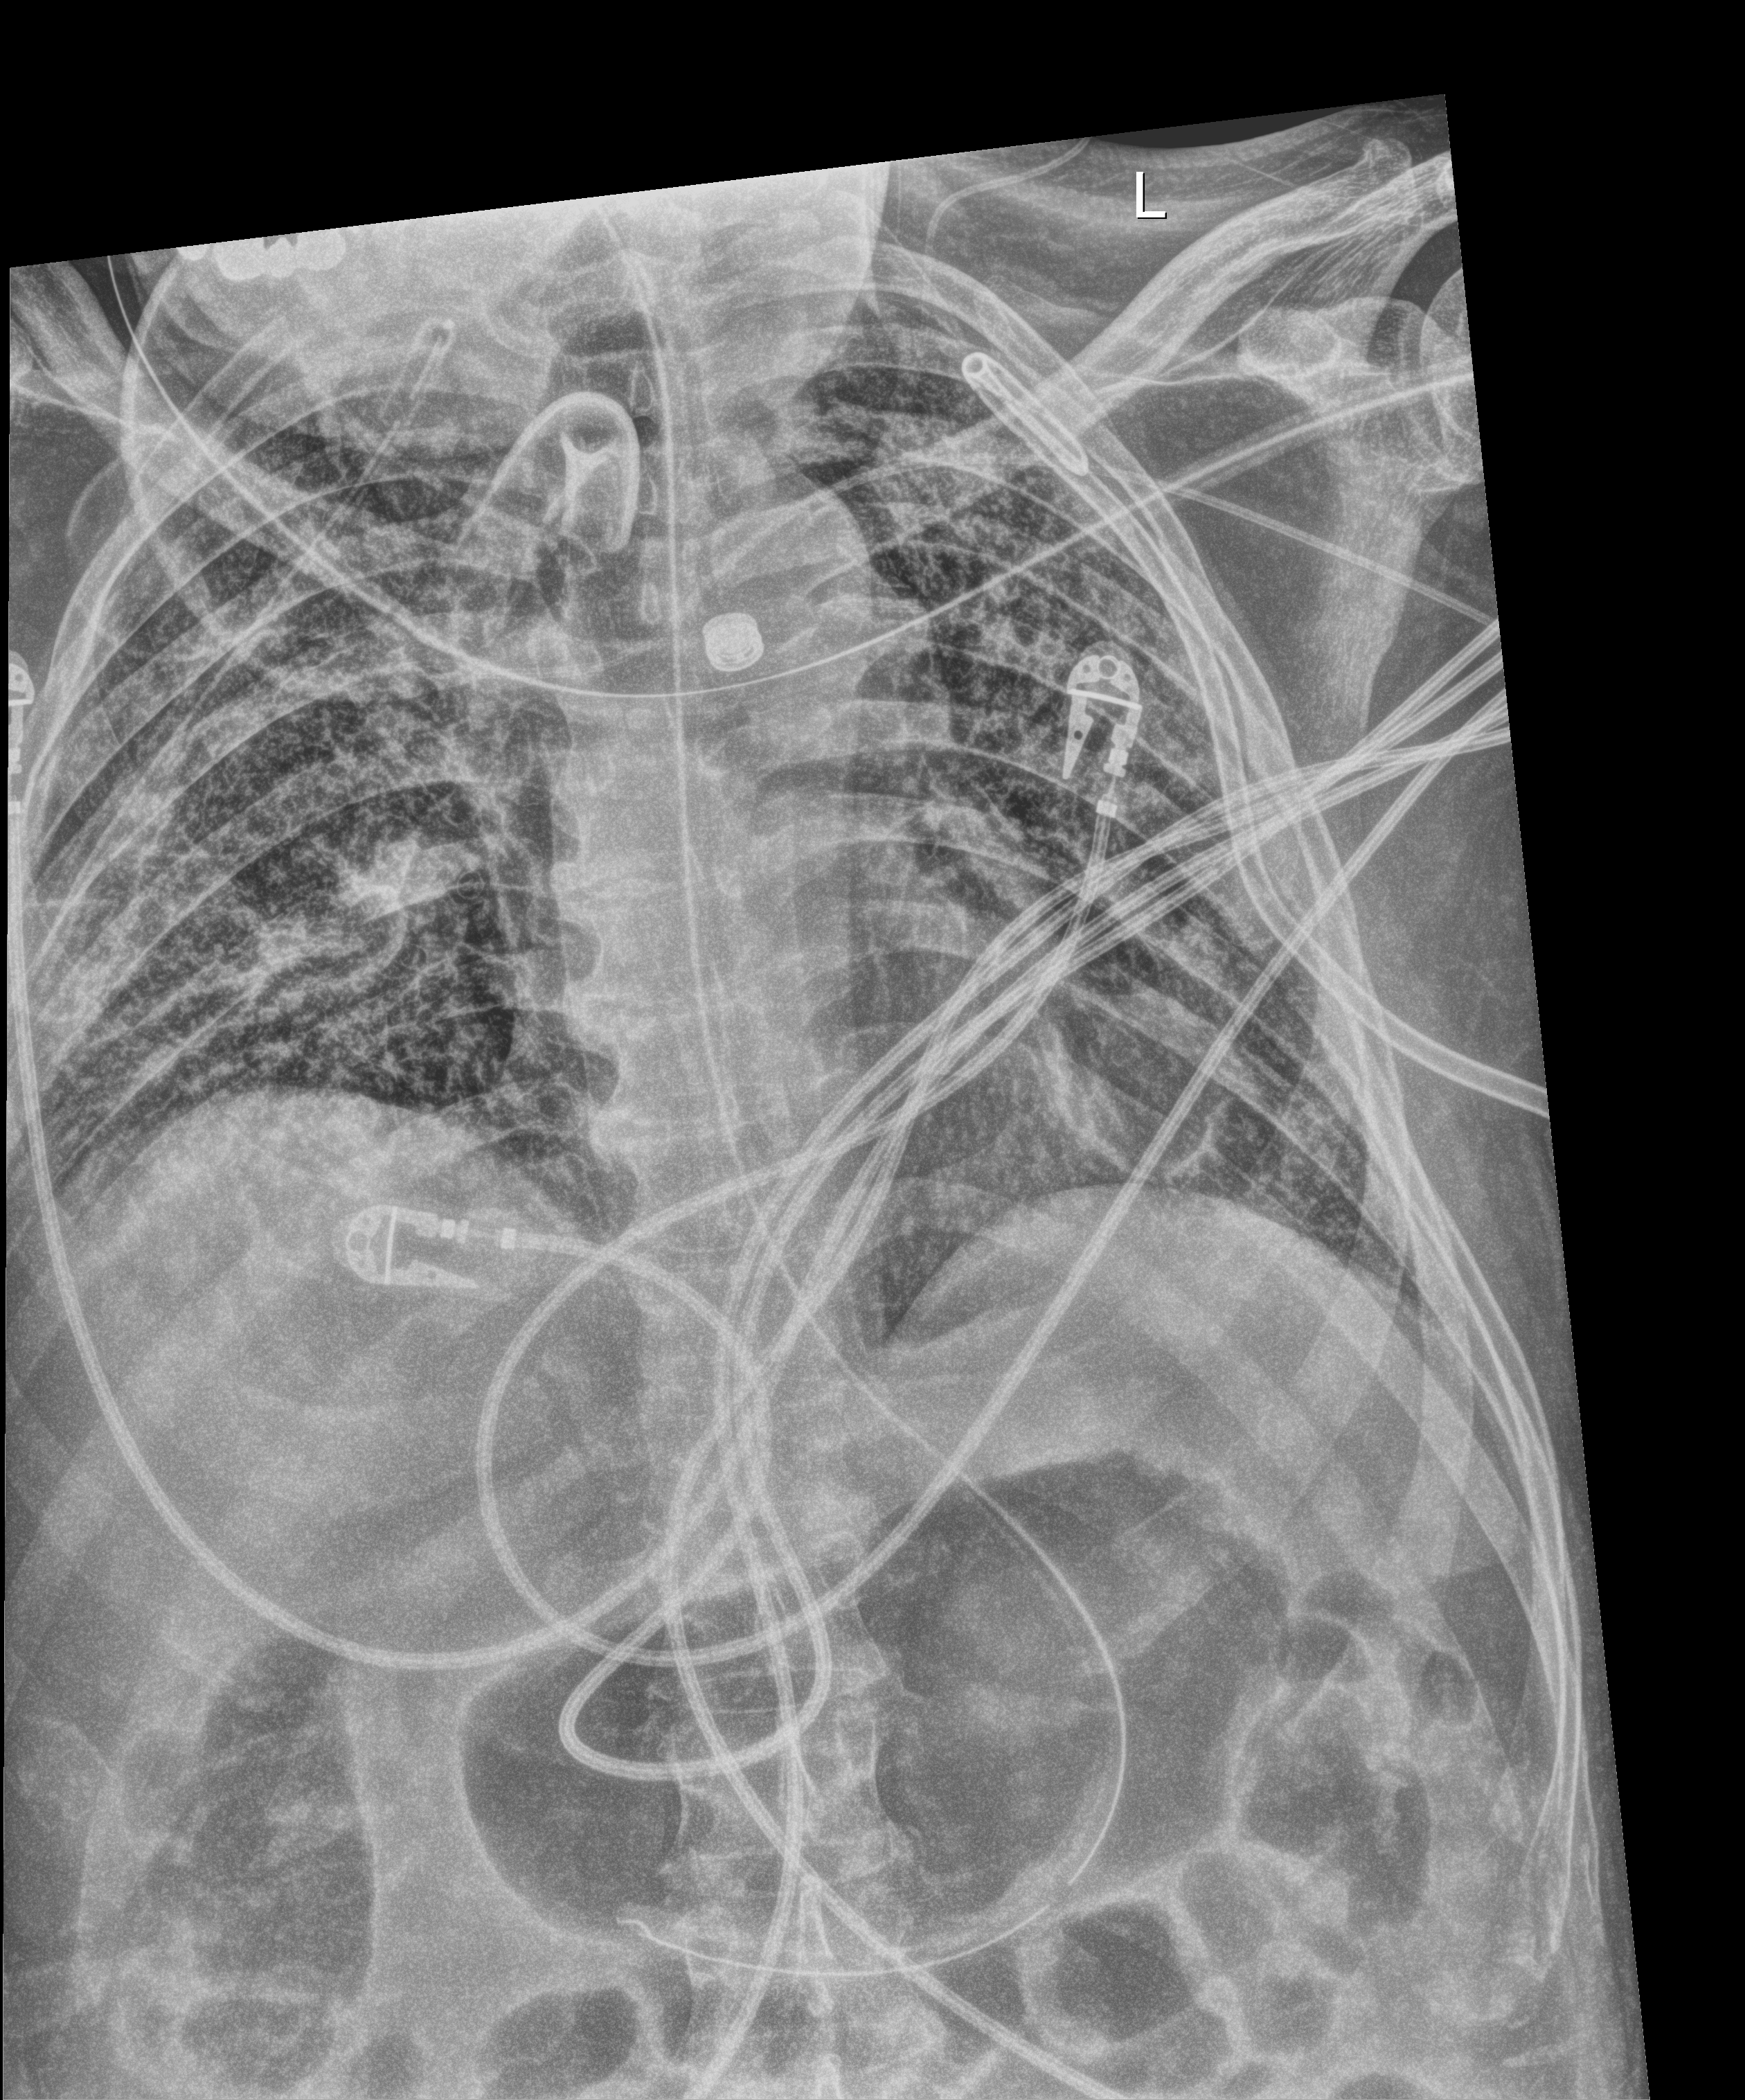
Bedside chest radiograph (digital radiography), anteroposterior (AP) projection. Male patient hospitalised with COVID-19, age 18–59 years.
From the hospital-stay record, not from the radiograph (when in the stay this image was taken is not recorded): other chronic lung disease (admission record): no.